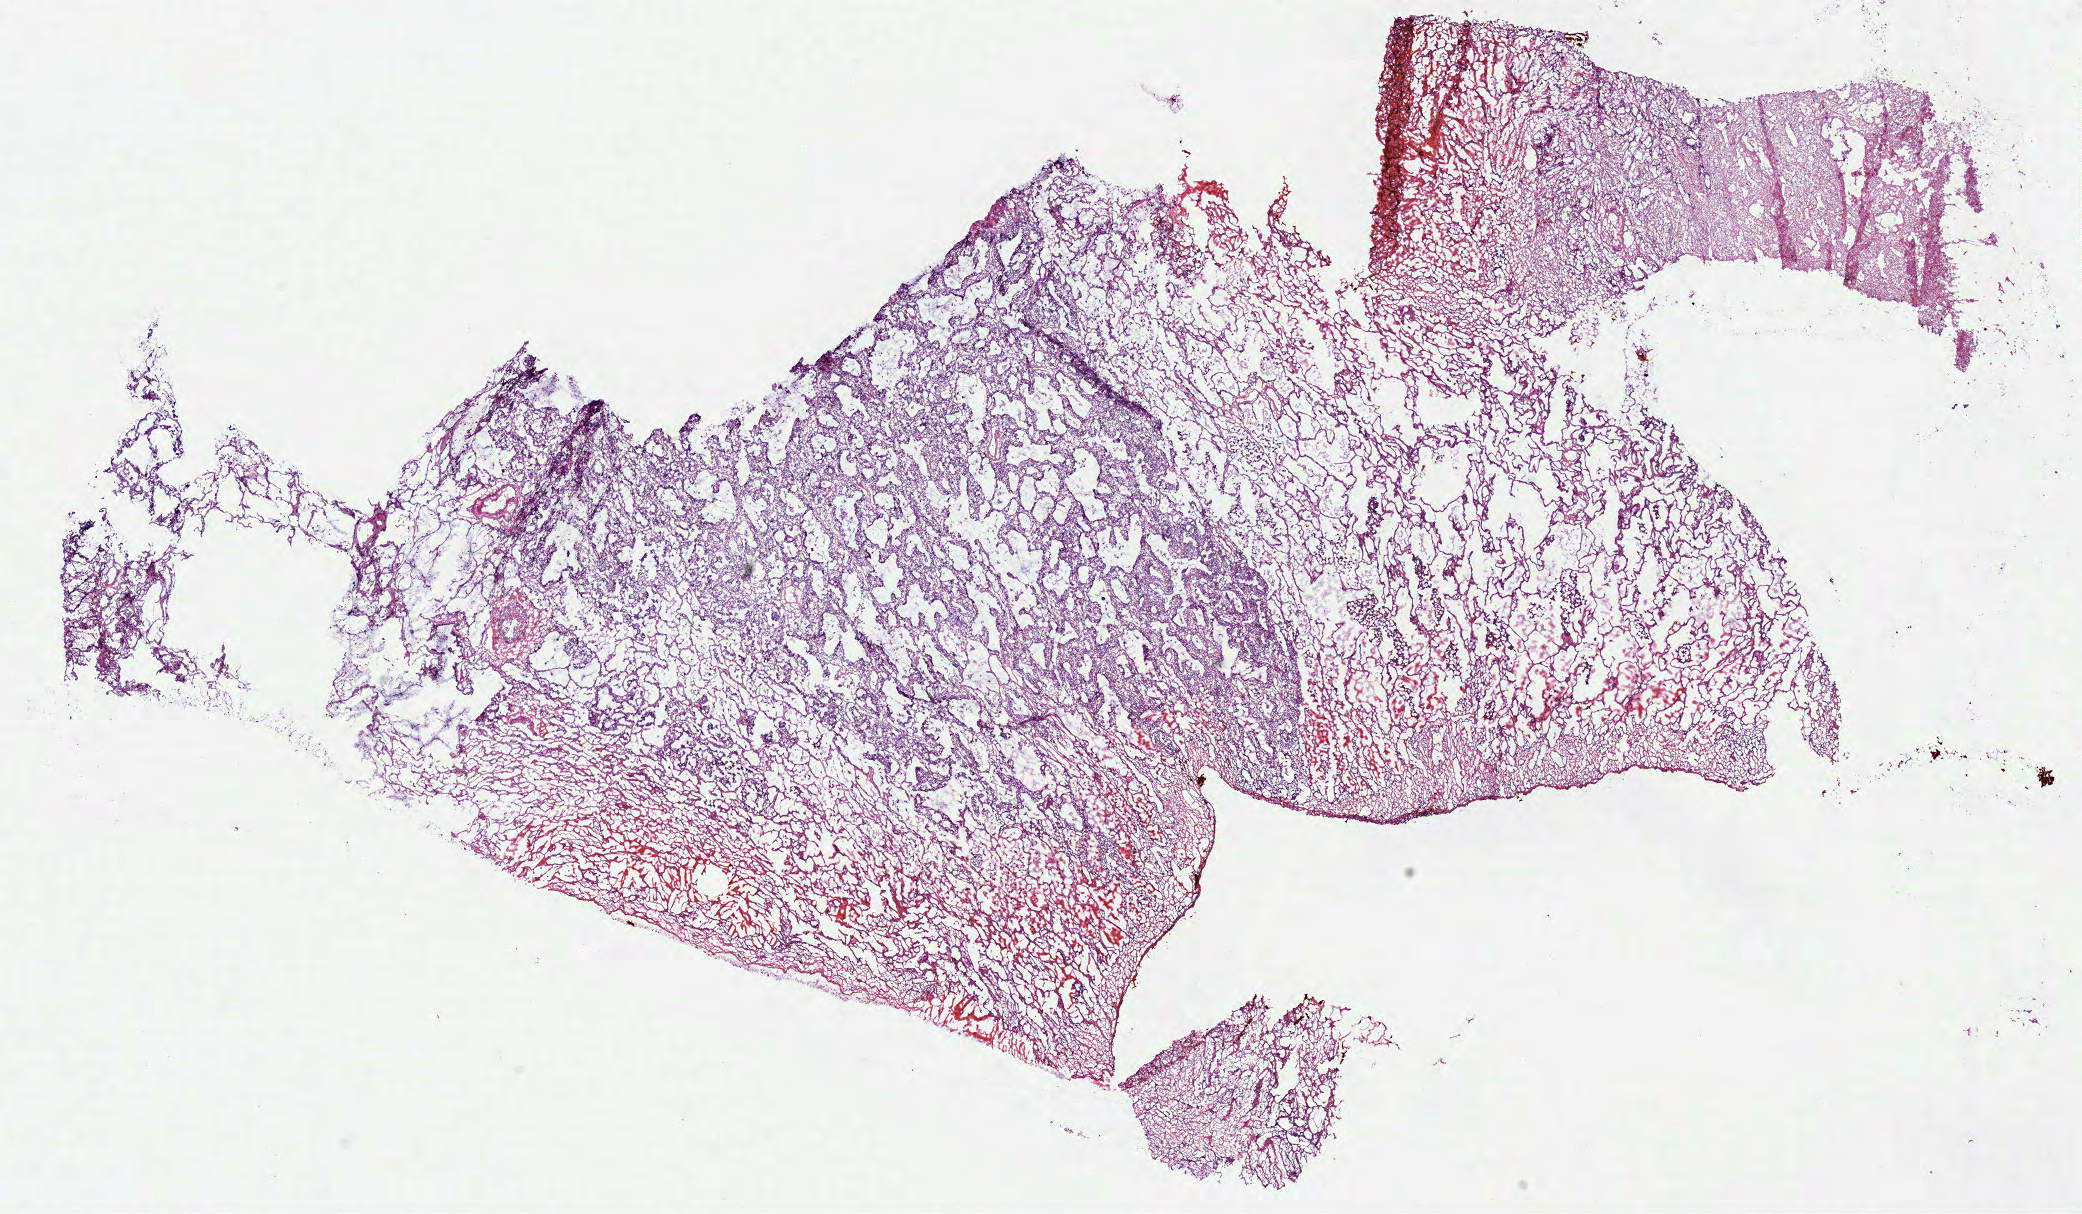
Whole-slide histology image, Hematoxylin and eosin (H&E) stained — shown as a low-resolution overview of the whole scanned area (about 16.4 x 9.6 mm). Frozen section from the top of the tissue portion. Lung, primary tumour sample. Male patient; age at initial diagnosis 70 years. Slide review estimates, as recorded: tumour cells 60%, tumour nuclei 60%, normal cells 25%, stromal cells 15%, necrosis 0%.
• histologic diagnosis: Mucinous adenocarcinoma (upper lobe, lung)
• AJCC pathologic stage: IIA (7th edition)